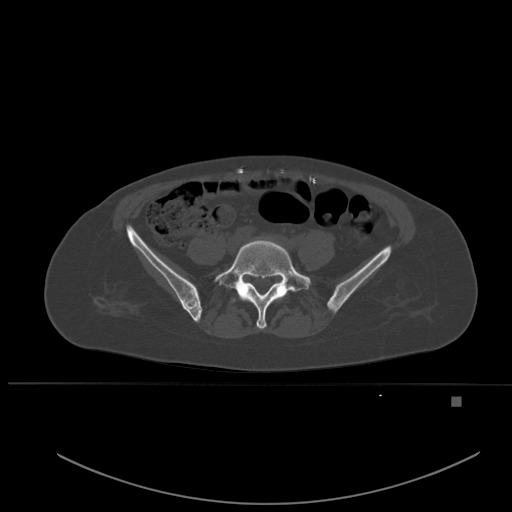
CT including the spine, one axial slice. Bone window (W 1800 / L 400 HU). 512 × 512 image matrix, field of view 443 × 443 mm. Female patient, age 49 years. From the clinical record (not read from this slice): primary cancer: breast; vertebrae with lytic lesions (as recorded): L3, T12, L4.
Annotated regions visible in this slice (semi-automatically segmented with operator editing):
- L5 vertebra: bounding box (x1, y1, x2, y2) in pixels: (214, 240, 311, 329)